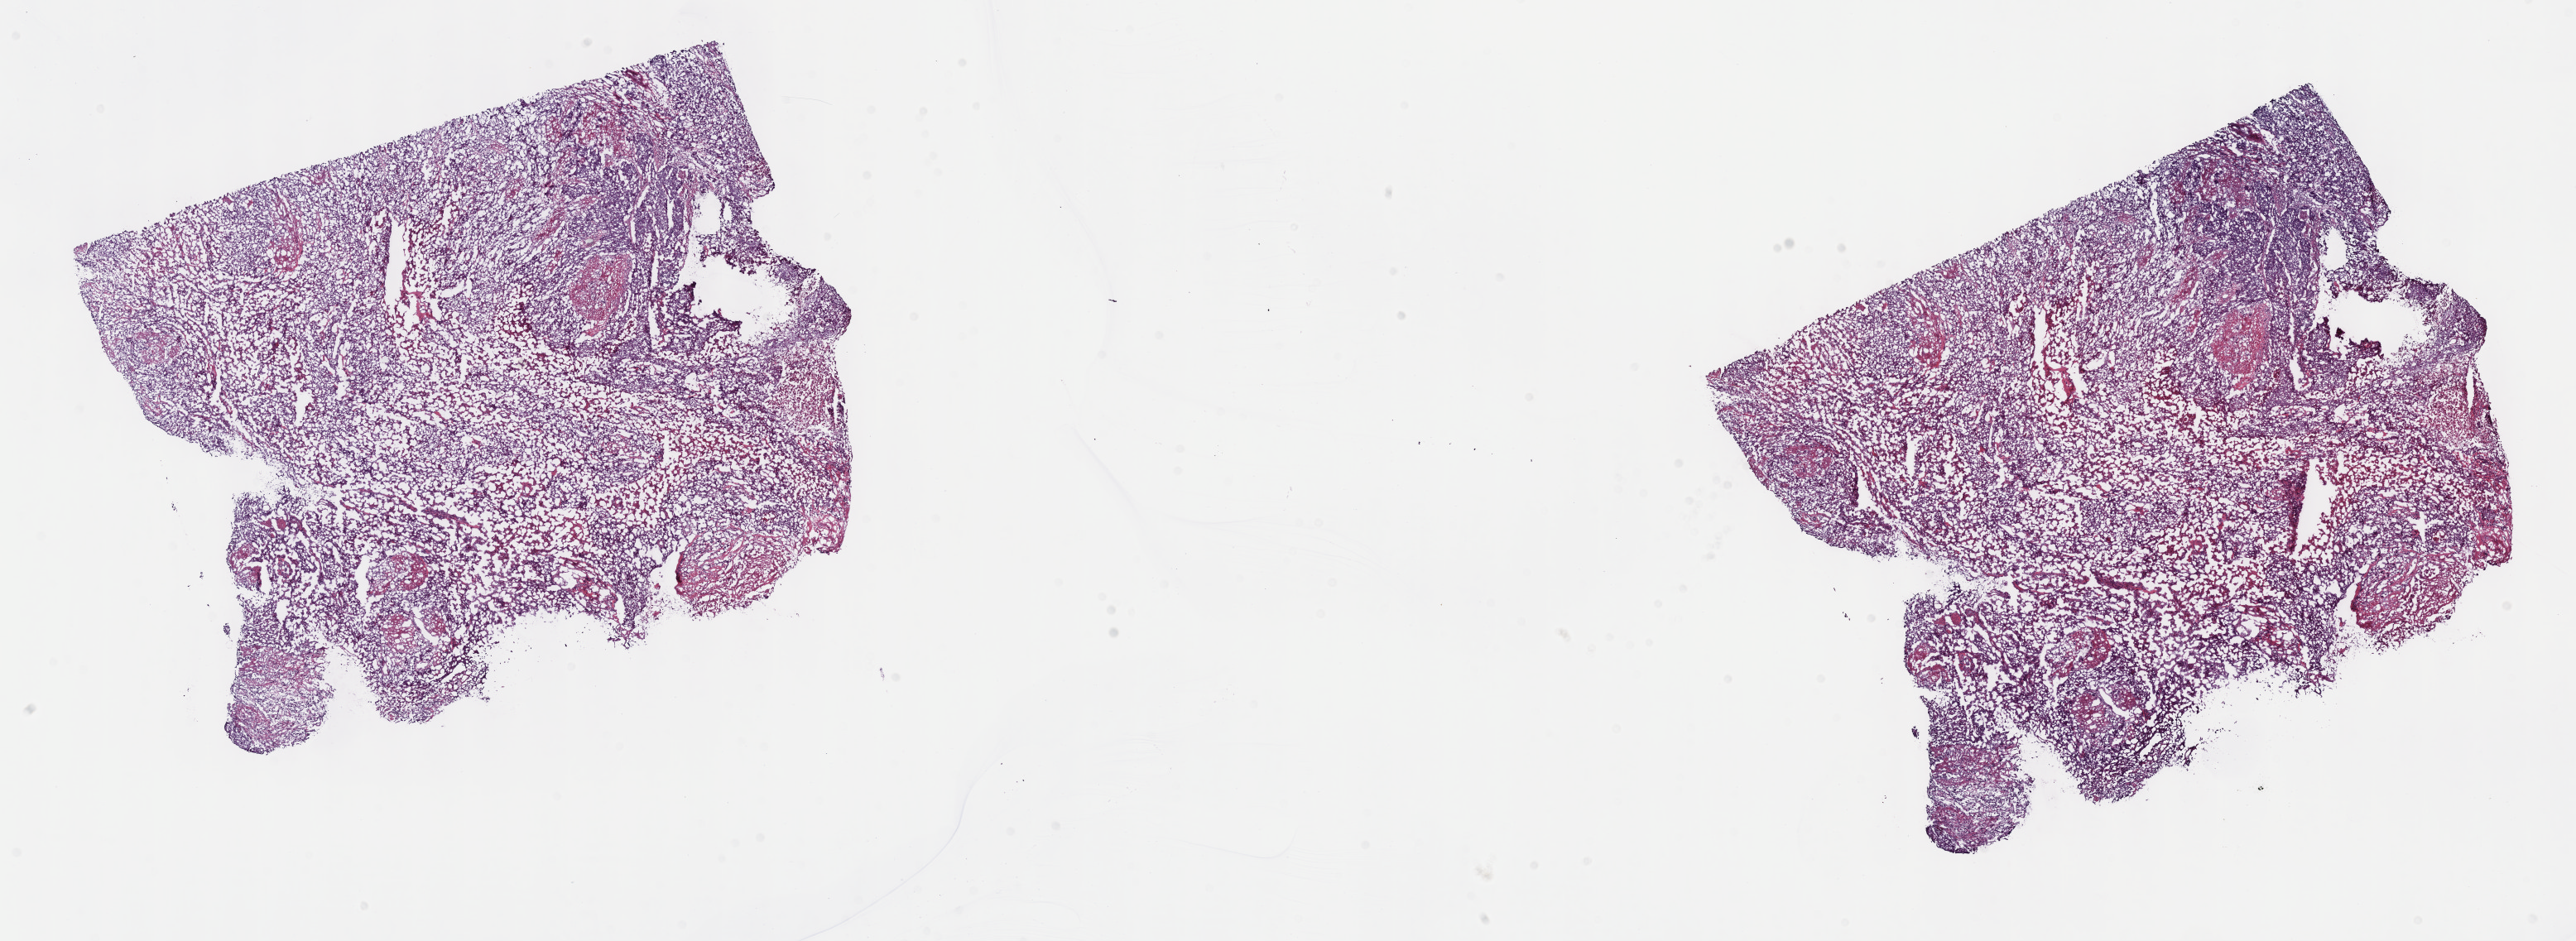
Digitized H&E-stained tissue section (whole slide), whole scanned area (about 25.2 x 9.2 mm, from a 40x scan) shown as a low-resolution overview. Frozen section from the top of the tissue portion. Sample: primary tumour, bladder. Male patient; age at initial diagnosis 68 years. Pathologist review of this section (percent, as recorded): tumour cells 100%, tumour nuclei 80%.
Diagnosis: Transitional cell carcinoma (lateral wall of bladder).